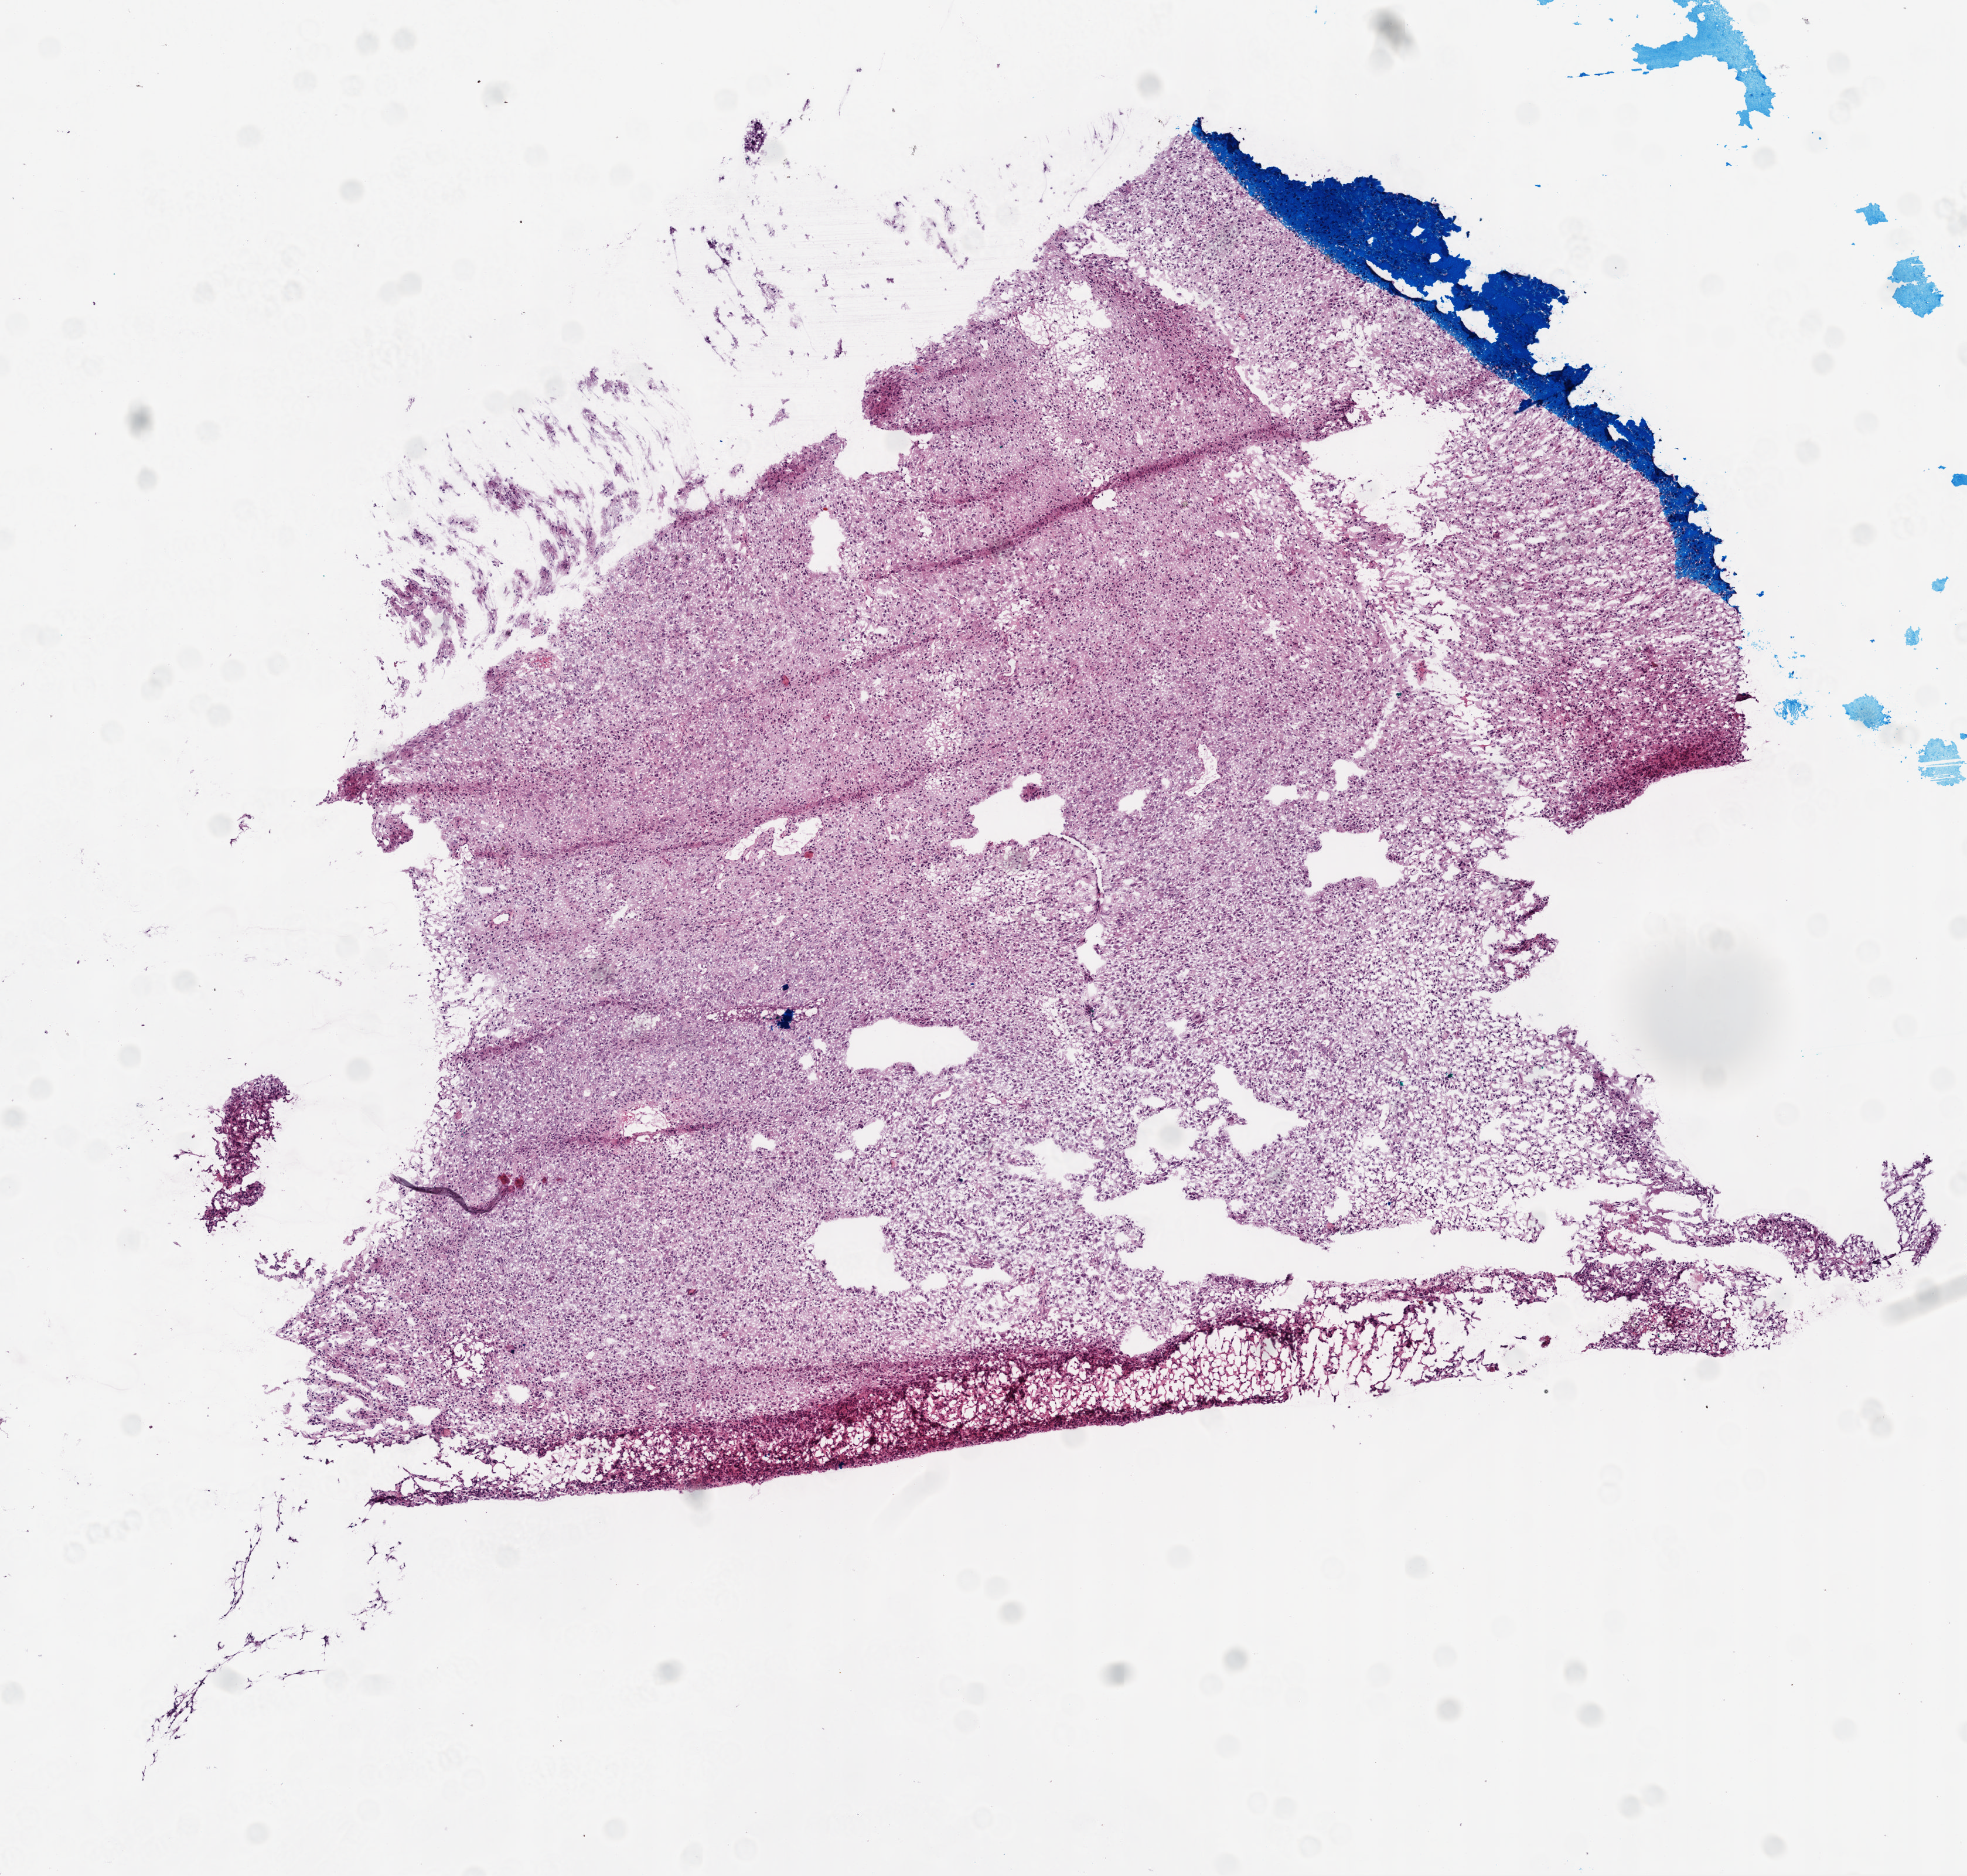
Whole-slide histology image, H&E, a low-resolution overview of the entire scanned area, about 6.8 x 6.5 mm, frozen section, brain, primary tumour sample. Patient: male, age at initial diagnosis 75 years. Slide review estimates, as recorded: tumour cells 100%, tumour nuclei 100%, normal cells 0%, stromal cells 0%, necrosis 0%.
• pathologic diagnosis: Glioblastoma